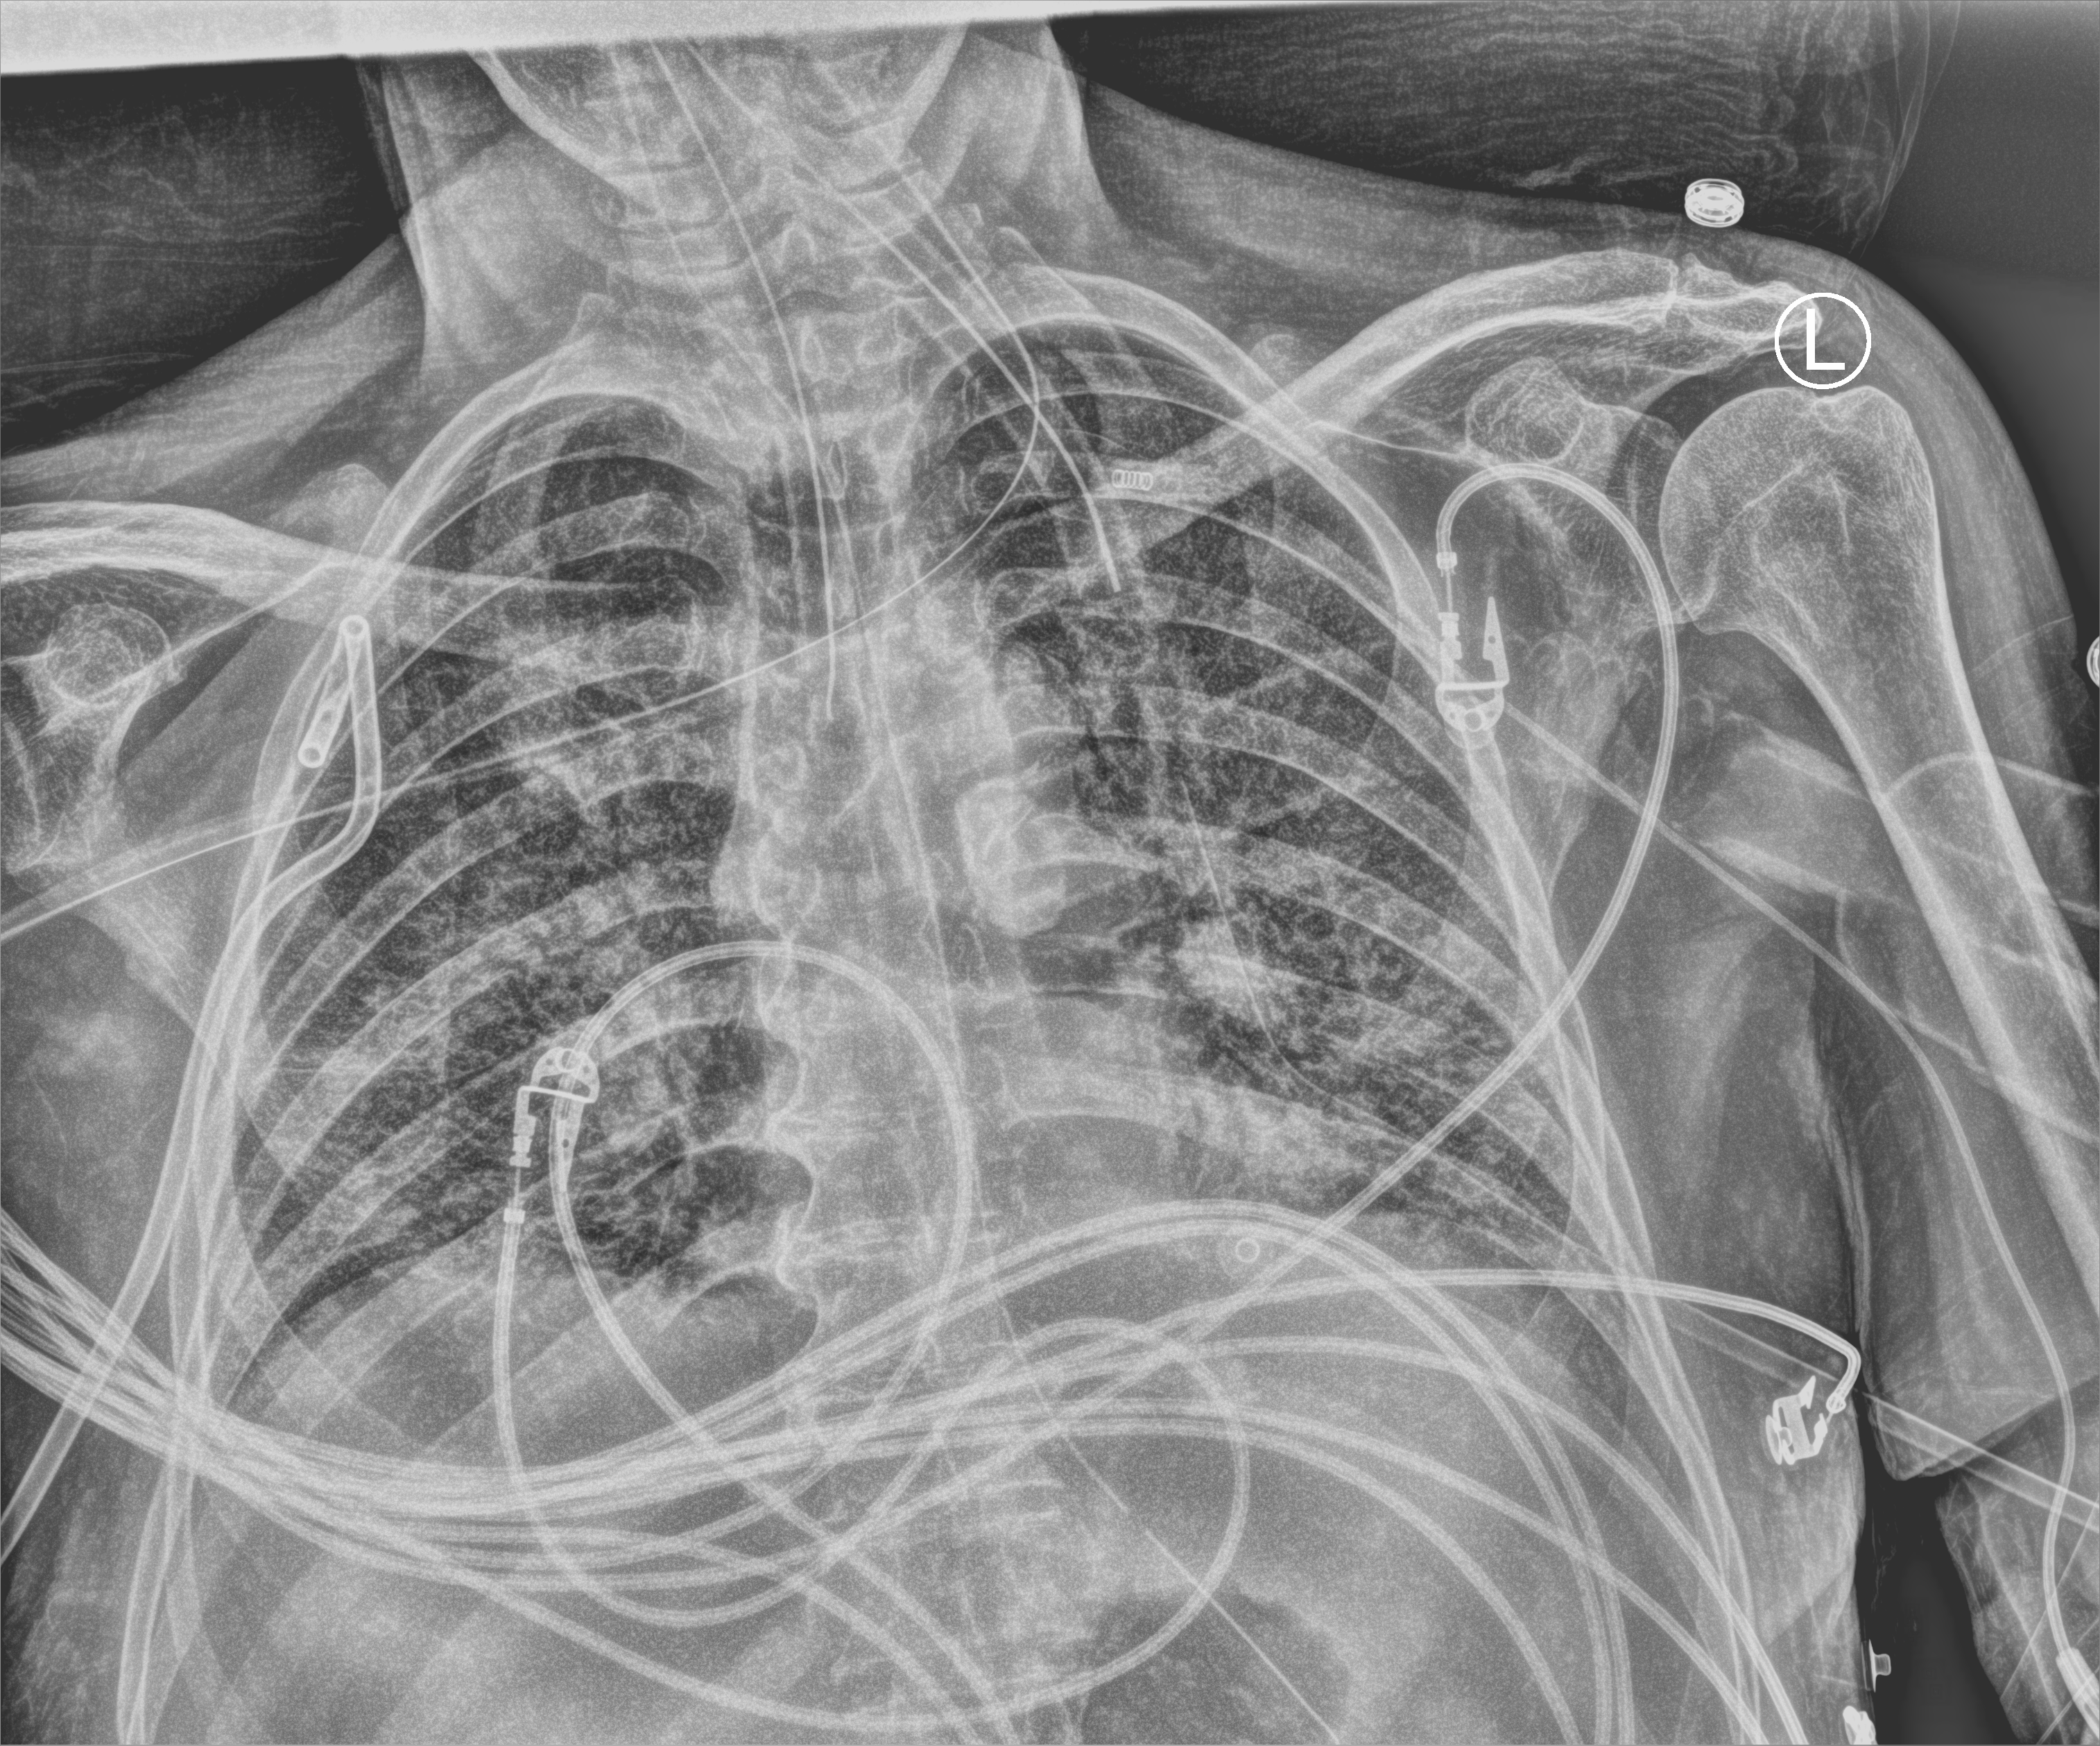
Portable chest radiograph; anteroposterior (AP) projection. Male patient hospitalised with COVID-19, age 75–90 years.
Admission-level facts for this patient (not findings on this image; timing relative to this image not recorded):
- mechanically ventilated during this hospital stay: yes